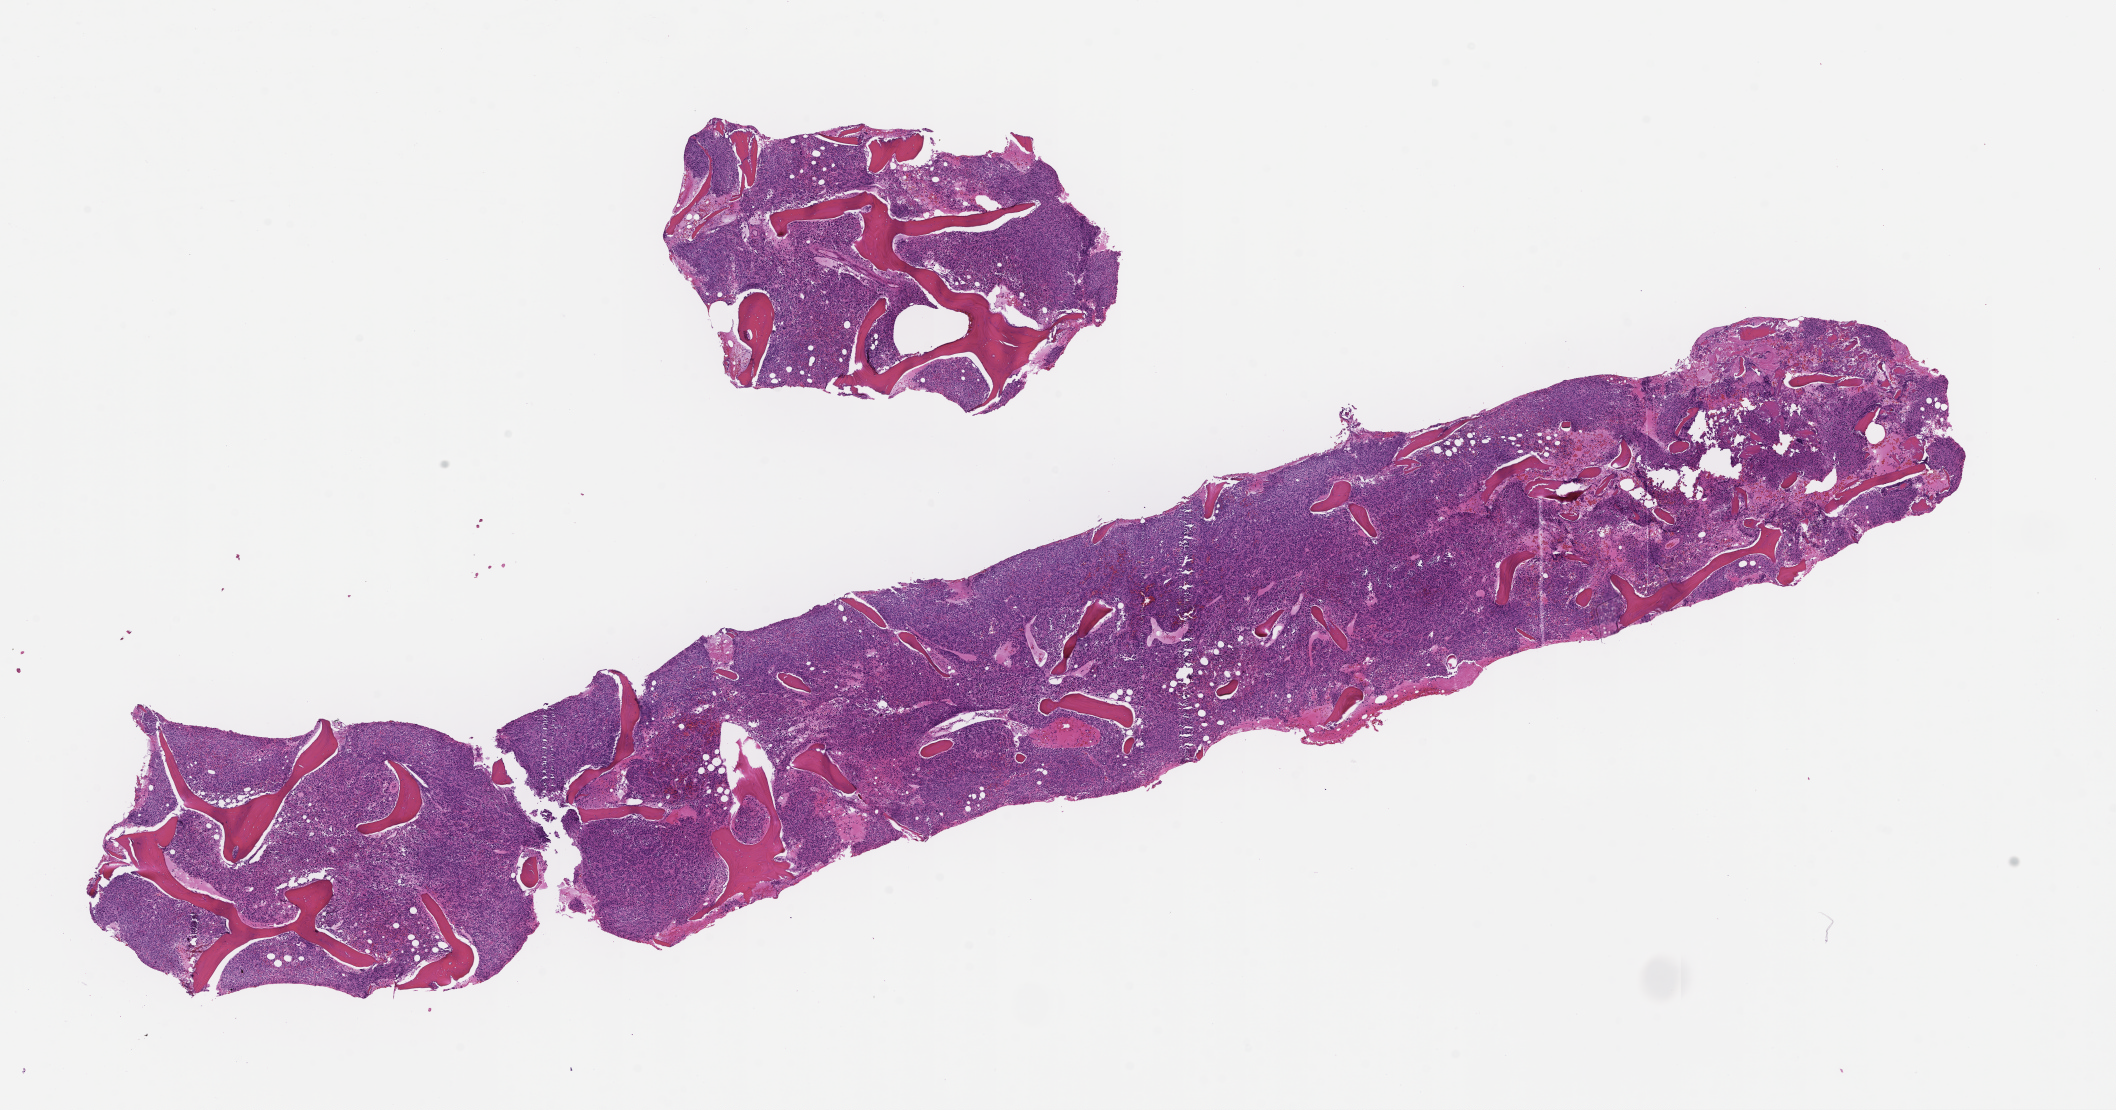
Digitized haematoxylin and eosin-stained section, a low-resolution overview of the entire scanned area, about 17.1 x 9.0 mm, FFPE section, archival tissue. Female patient.
This section: metastasis (sampled organ not recorded). Primary diagnosis of the patient: Small Cell Lung Carcinoma.